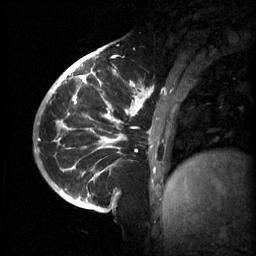
Breast MRI (dynamic contrast-enhanced), one sagittal slice. Position 18 of 60 along the scan axis. 3 images stored at this slice position (order not interpretable as contrast timing). 1.5 T. TE 4.2 ms, TR 11 ms. 2 mm slice thickness. 256 × 256 image matrix, field of view 220 × 220 mm. Patient: female, 51 years.
Outlined on this slice (semi-automatic segmentation, software-assisted and operator-edited):
- analysis volume of interest (the breast-tissue region the enhancement analysis was run in; not a lesion): bounding box (x1, y1, x2, y2) in pixels: (63, 80, 187, 201)
- tumour enhancement mask (voxels above the 70 % enhancement threshold inside the analysis volume of interest): (67, 80, 154, 183)